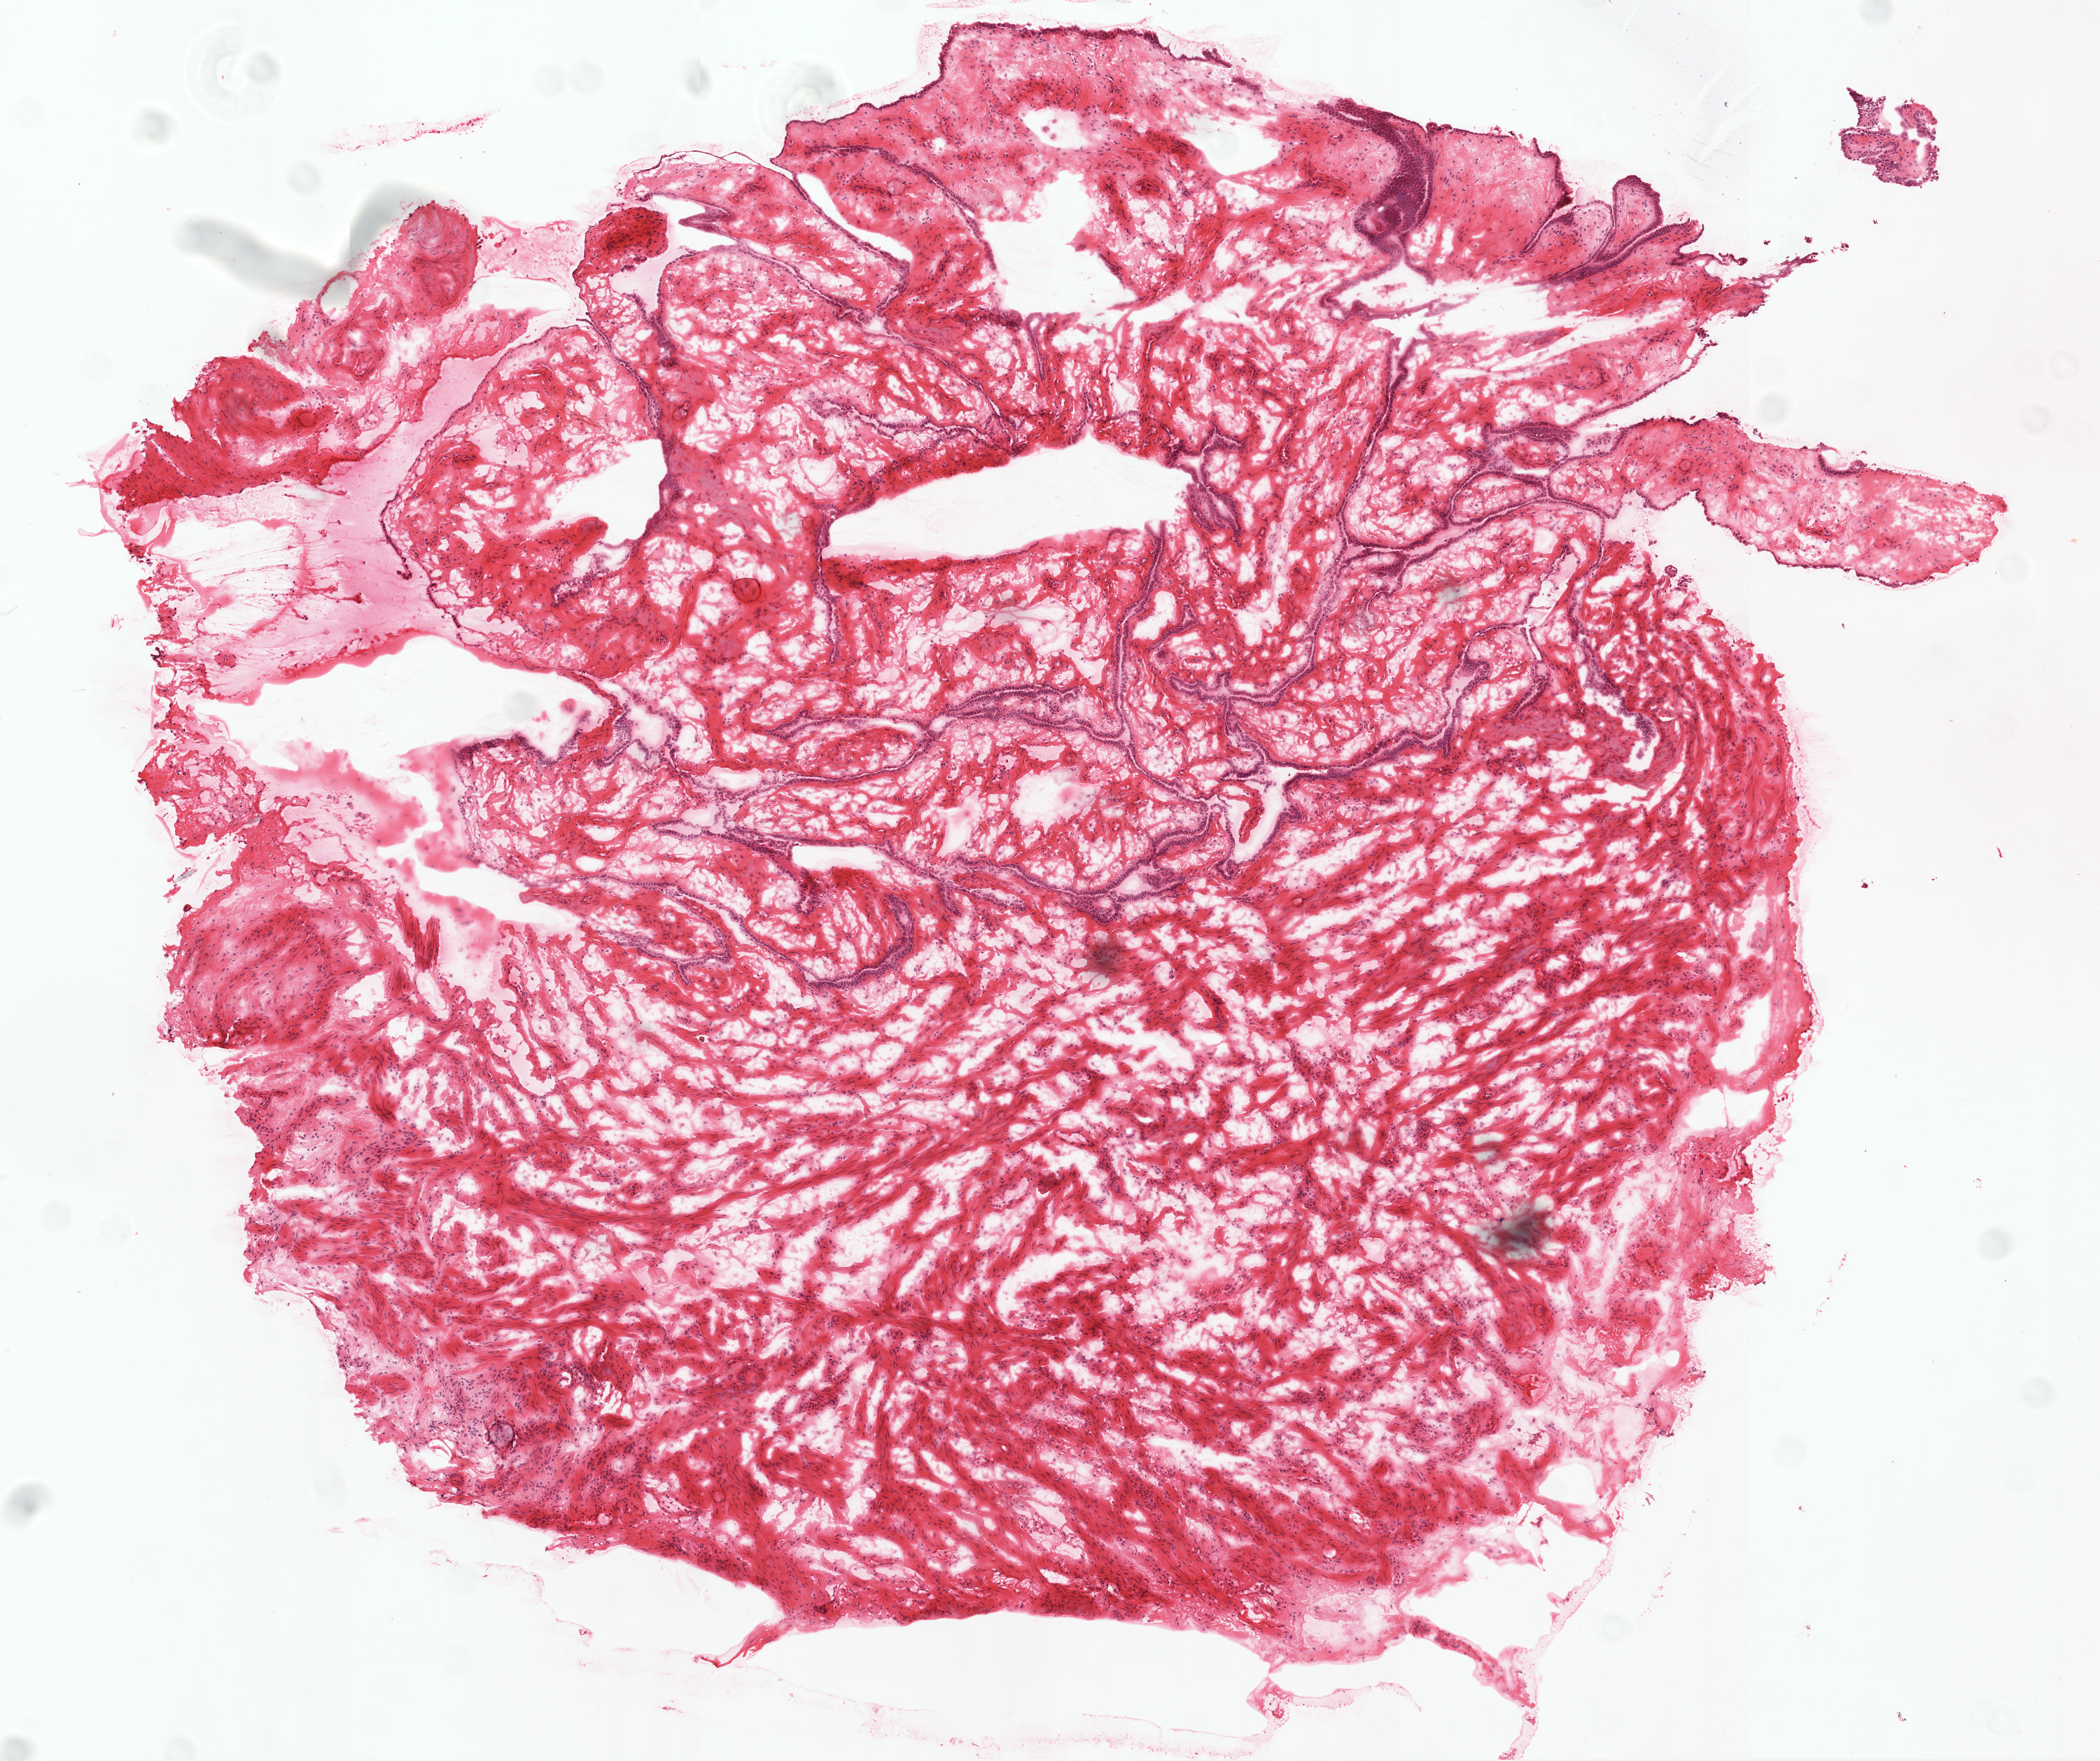
Whole-slide histology image, H&E, shown as a low-resolution overview of the whole scanned area (about 6.0 x 5.0 mm). Frozen section. Ovary, solid tissue normal (non-tumour tissue) sample. Female, age 74 years at initial diagnosis.
- this section: solid tissue normal sample (biorepository sample class)
- patient diagnosis: Serous cystadenocarcinoma, NOS